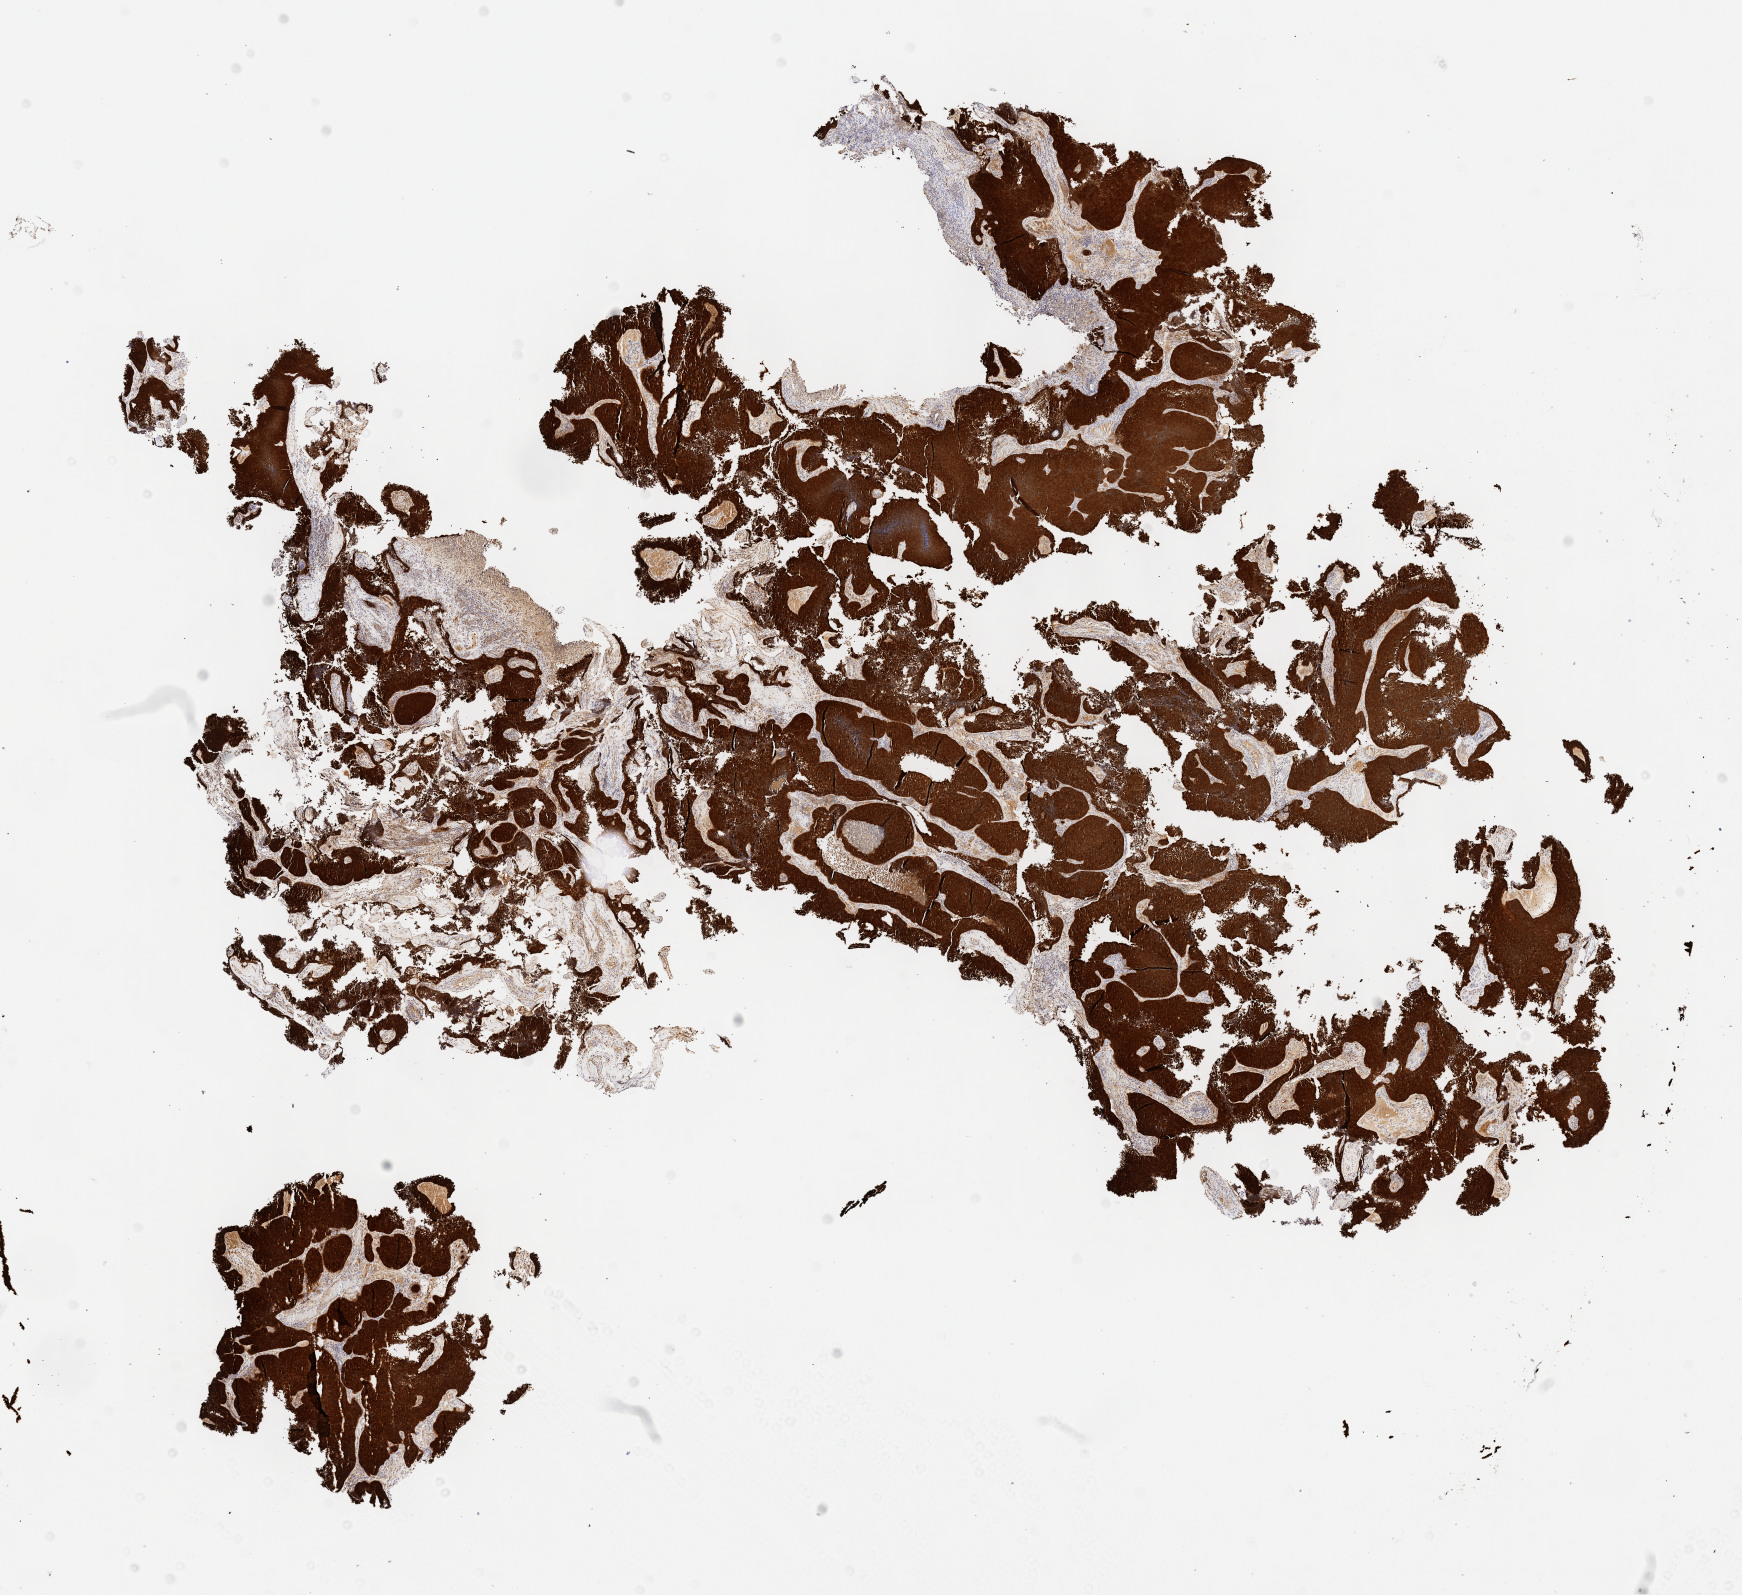
Immunohistochemistry (IHC) whole-slide image stained for p16 (p16INK4a), low-resolution overview of the scanned area, about 14.1 x 12.9 mm, tumor tissue, anatomic site: cervix. Patient female; aged 80.
* histologic diagnosis: Carcinoma, NOS